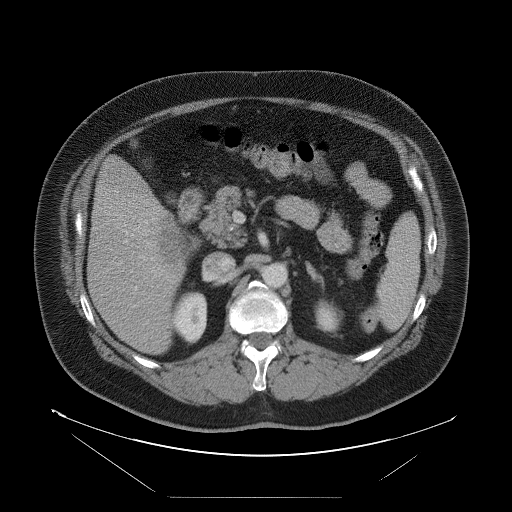
Contrast-enhanced abdominal CT, one axial slice; slice 45 of 114 in the series (ordered by position); 120 kVp; soft-tissue window (W 400 / L 40 HU); 512 × 512 image matrix, field of view 500 × 500 mm. Male patient, age 61 years. Case-level facts recorded for this patient, not image findings: diagnosis: colorectal cancer liver metastases, imaged before liver resection; multiple liver metastases: no; largest metastasis: 6.5 cm; chemotherapy before resection: no.
Outlined on this slice (outlined manually by an expert reader):
- liver: bounding box (x1, y1, x2, y2) in pixels: (89, 157, 190, 355)
- liver metastasis: (160, 217, 197, 268)